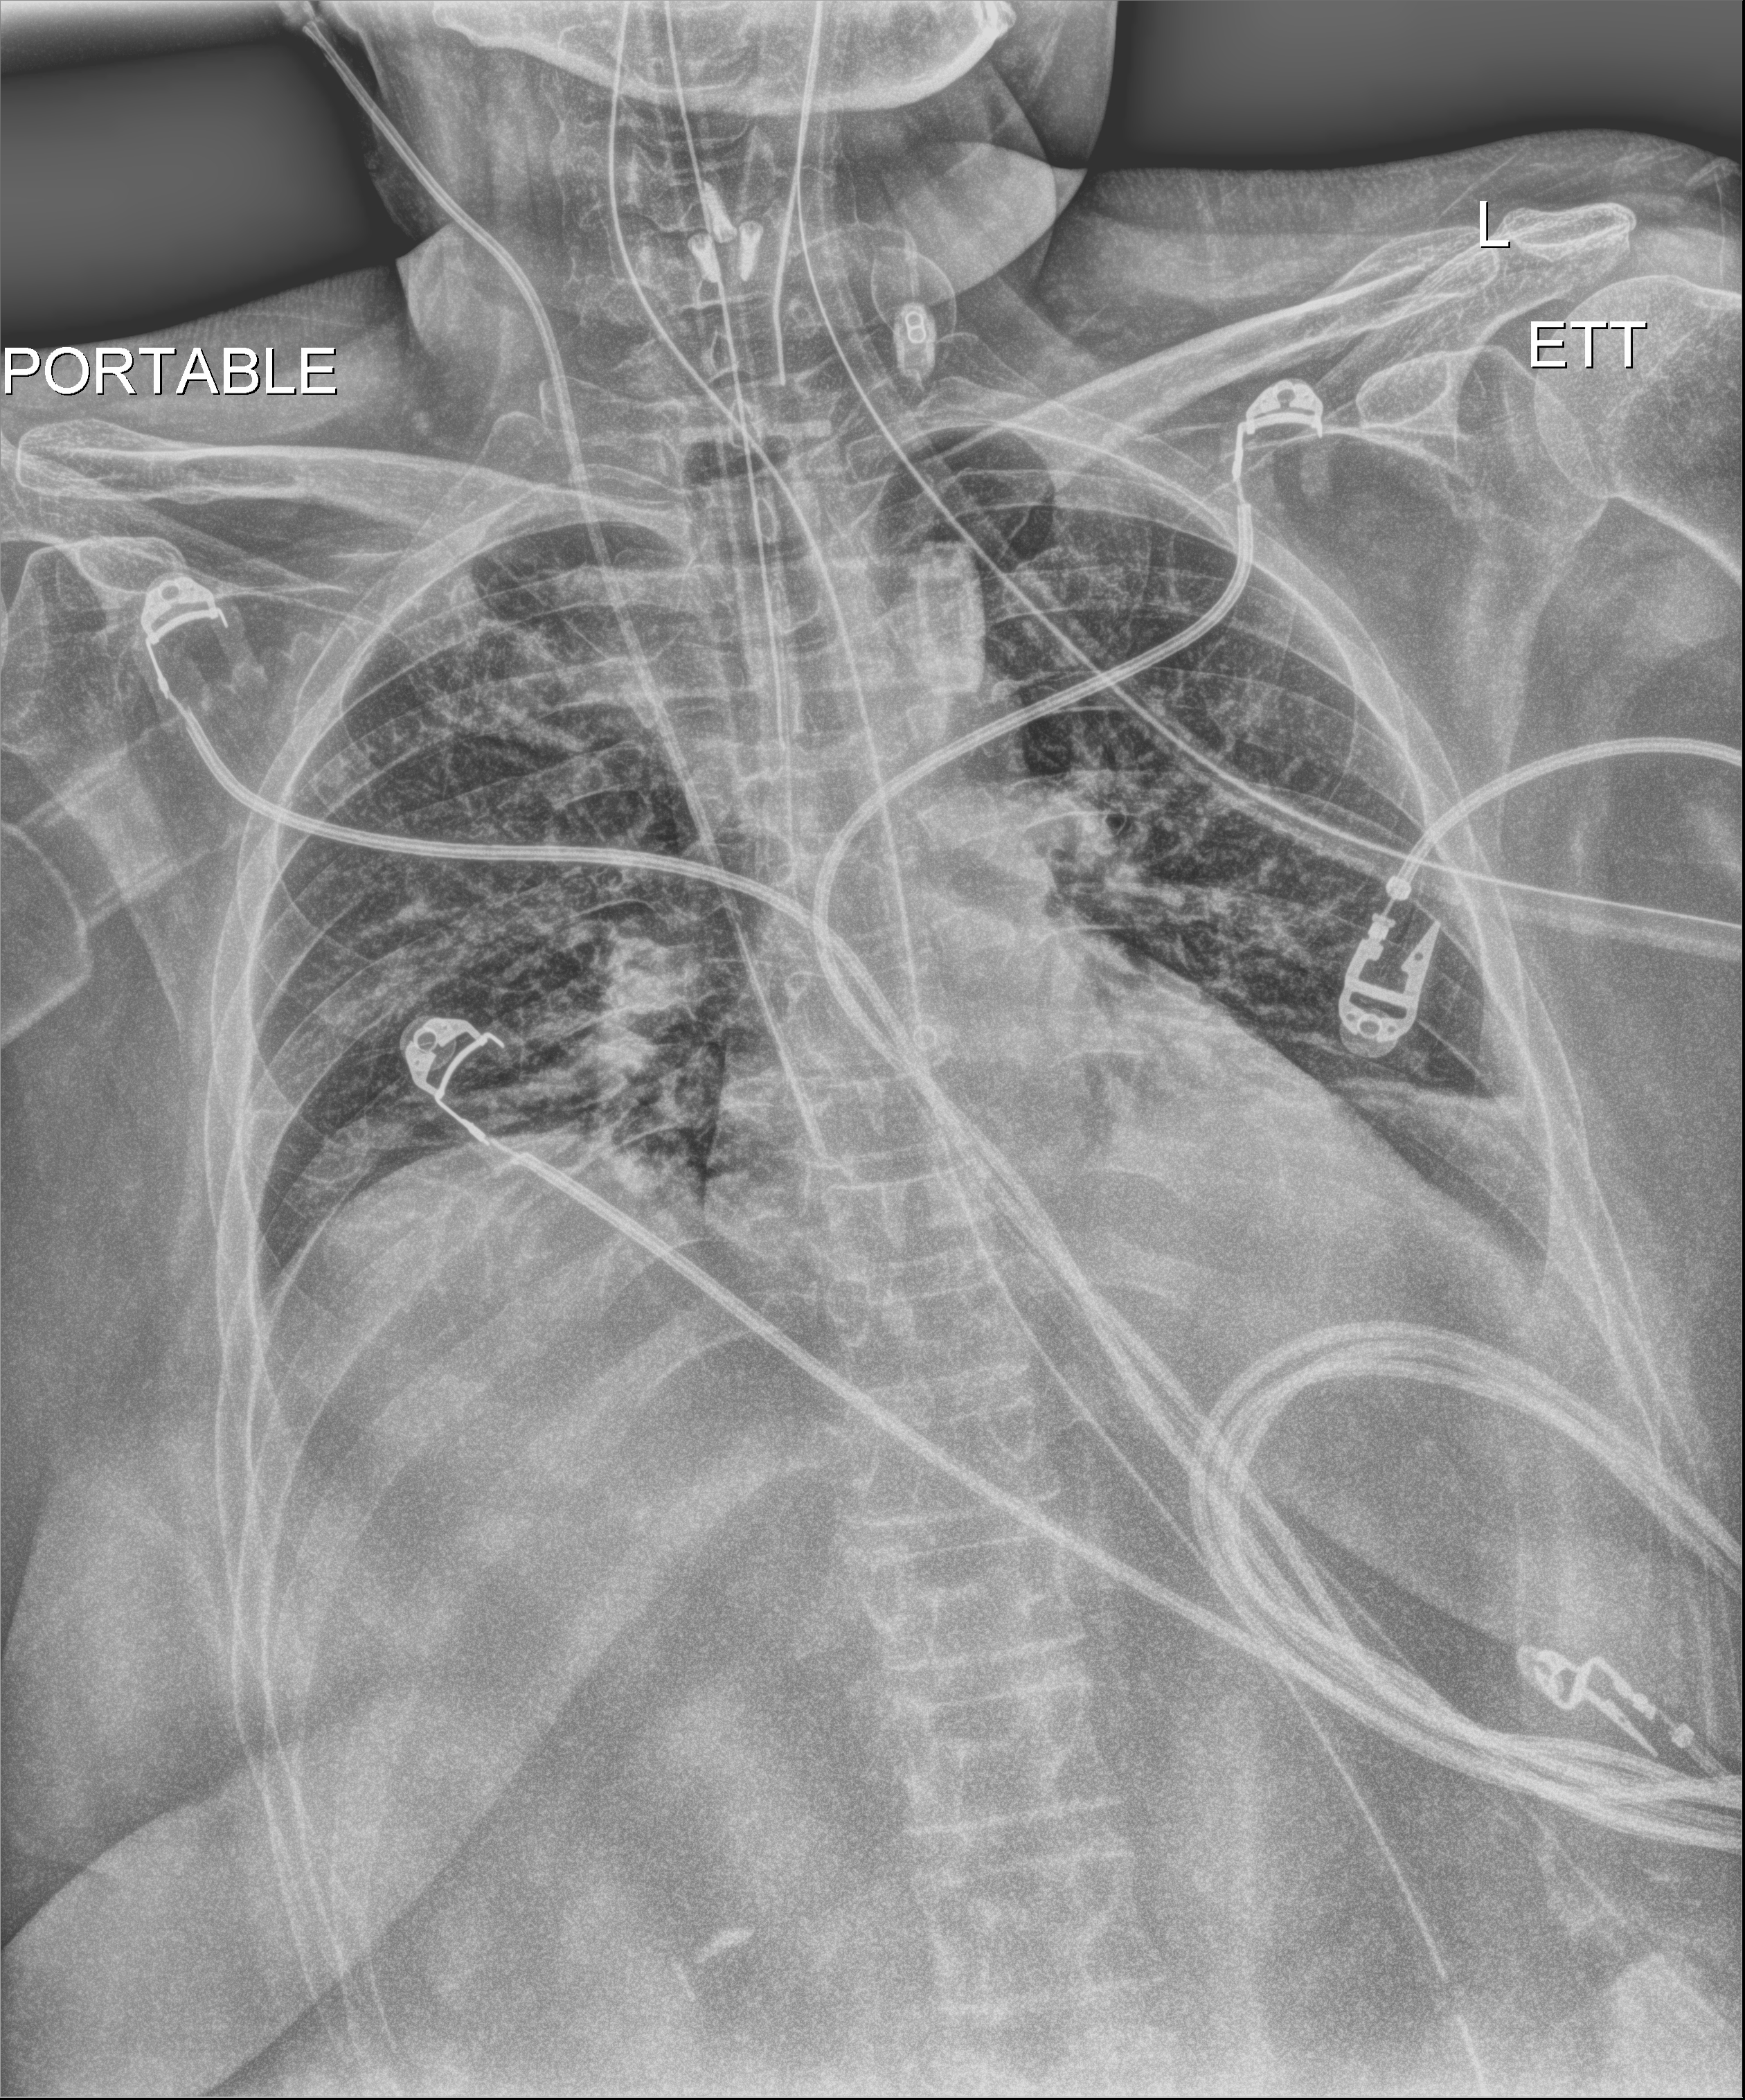
Portable chest radiograph; anteroposterior (AP) projection. Female patient hospitalised with COVID-19, age 18–59 years.
Admission-level facts for this patient (not findings on this image; timing relative to this image not recorded):
- length of hospital stay: 44 days
- mechanically ventilated during this hospital stay: no